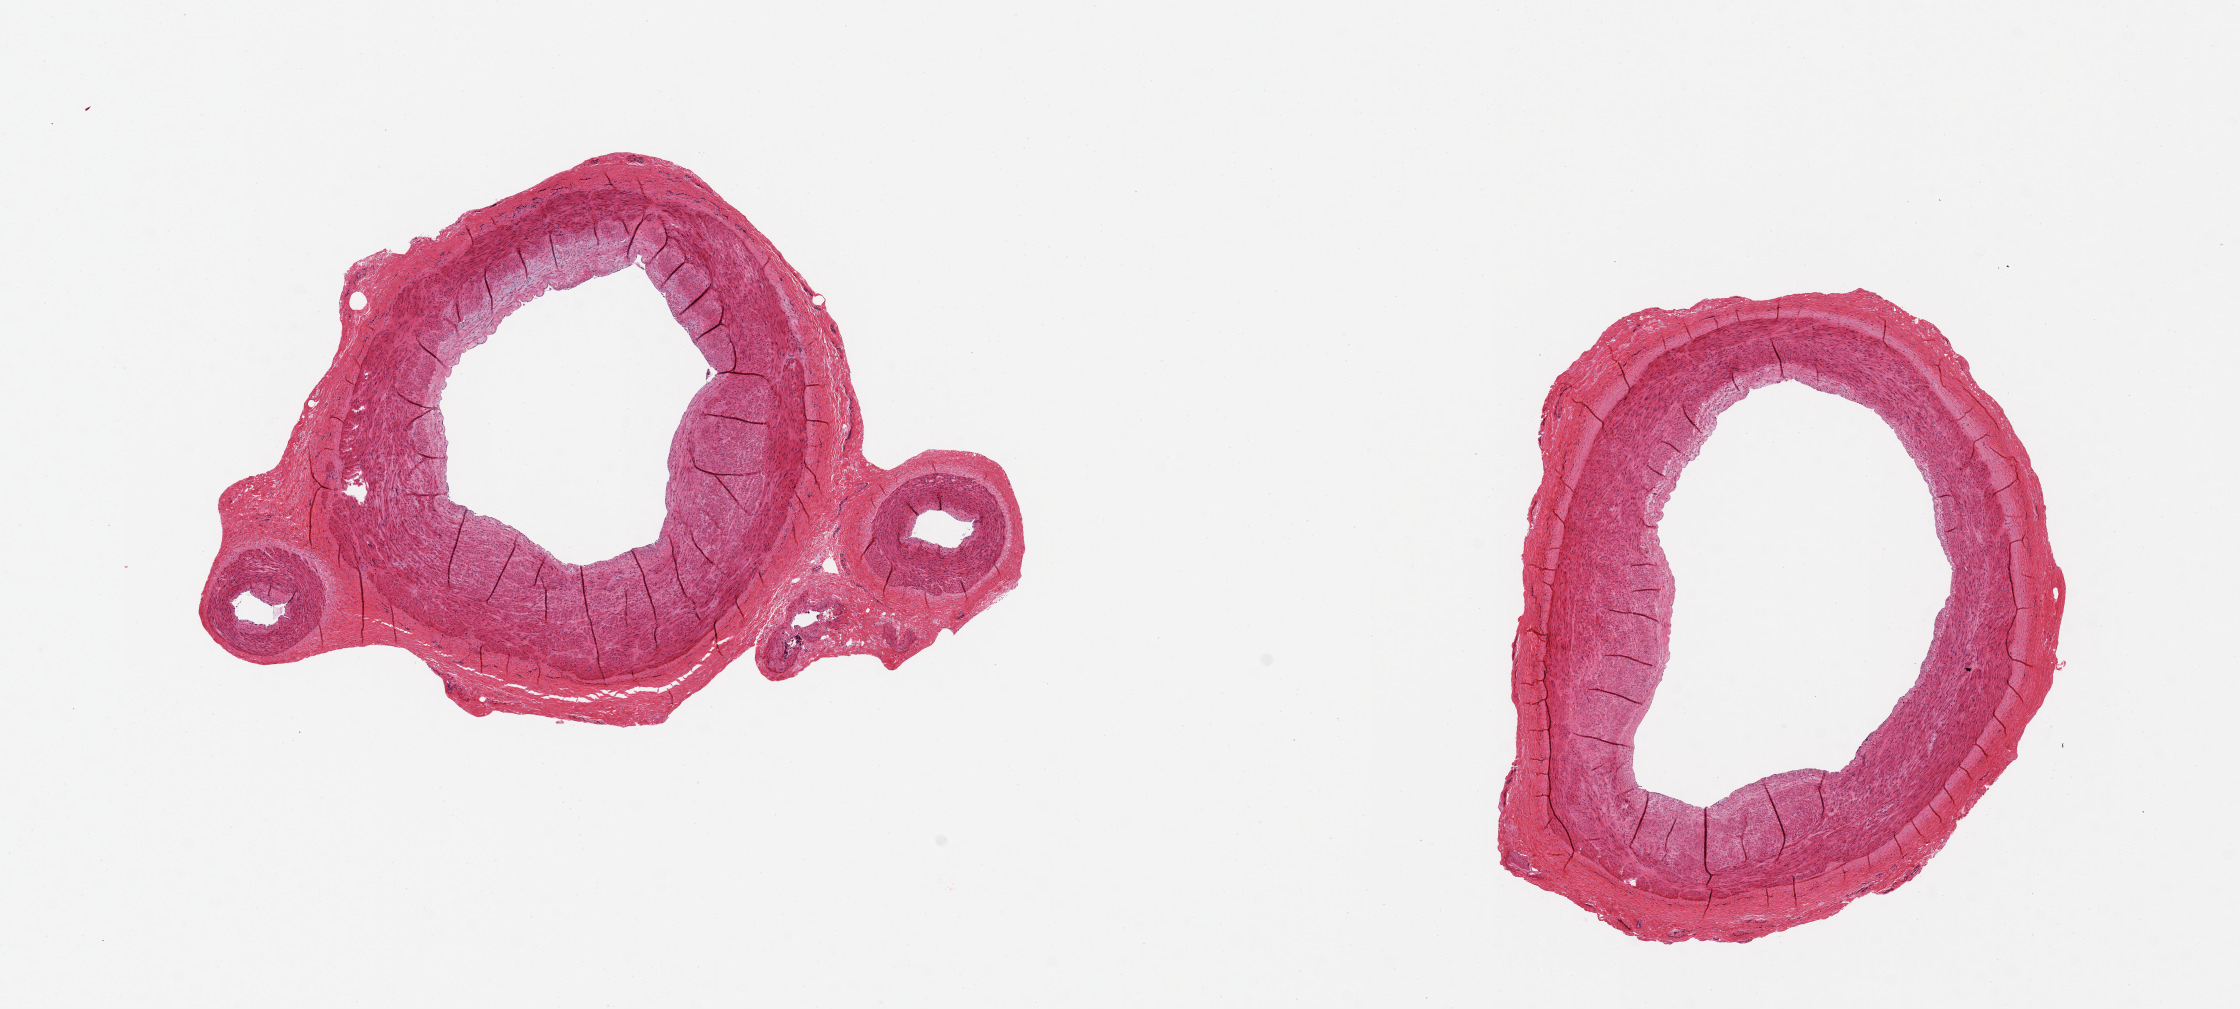
Whole-slide image, hematoxylin and eosin (H&E) stain — shown as a low-resolution overview of the whole scanned area (about 17.7 x 8.0 mm, slide scanned at 20x). PAXgene-fixed paraffin-embedded (PFPE) section. Target tissue: tibial artery. Tissue donor sample.
Review note (as recorded): 2 pieces ~5mm d; Excellent clean specimens; one aliquot with small branch arteries, suitable for analysis.